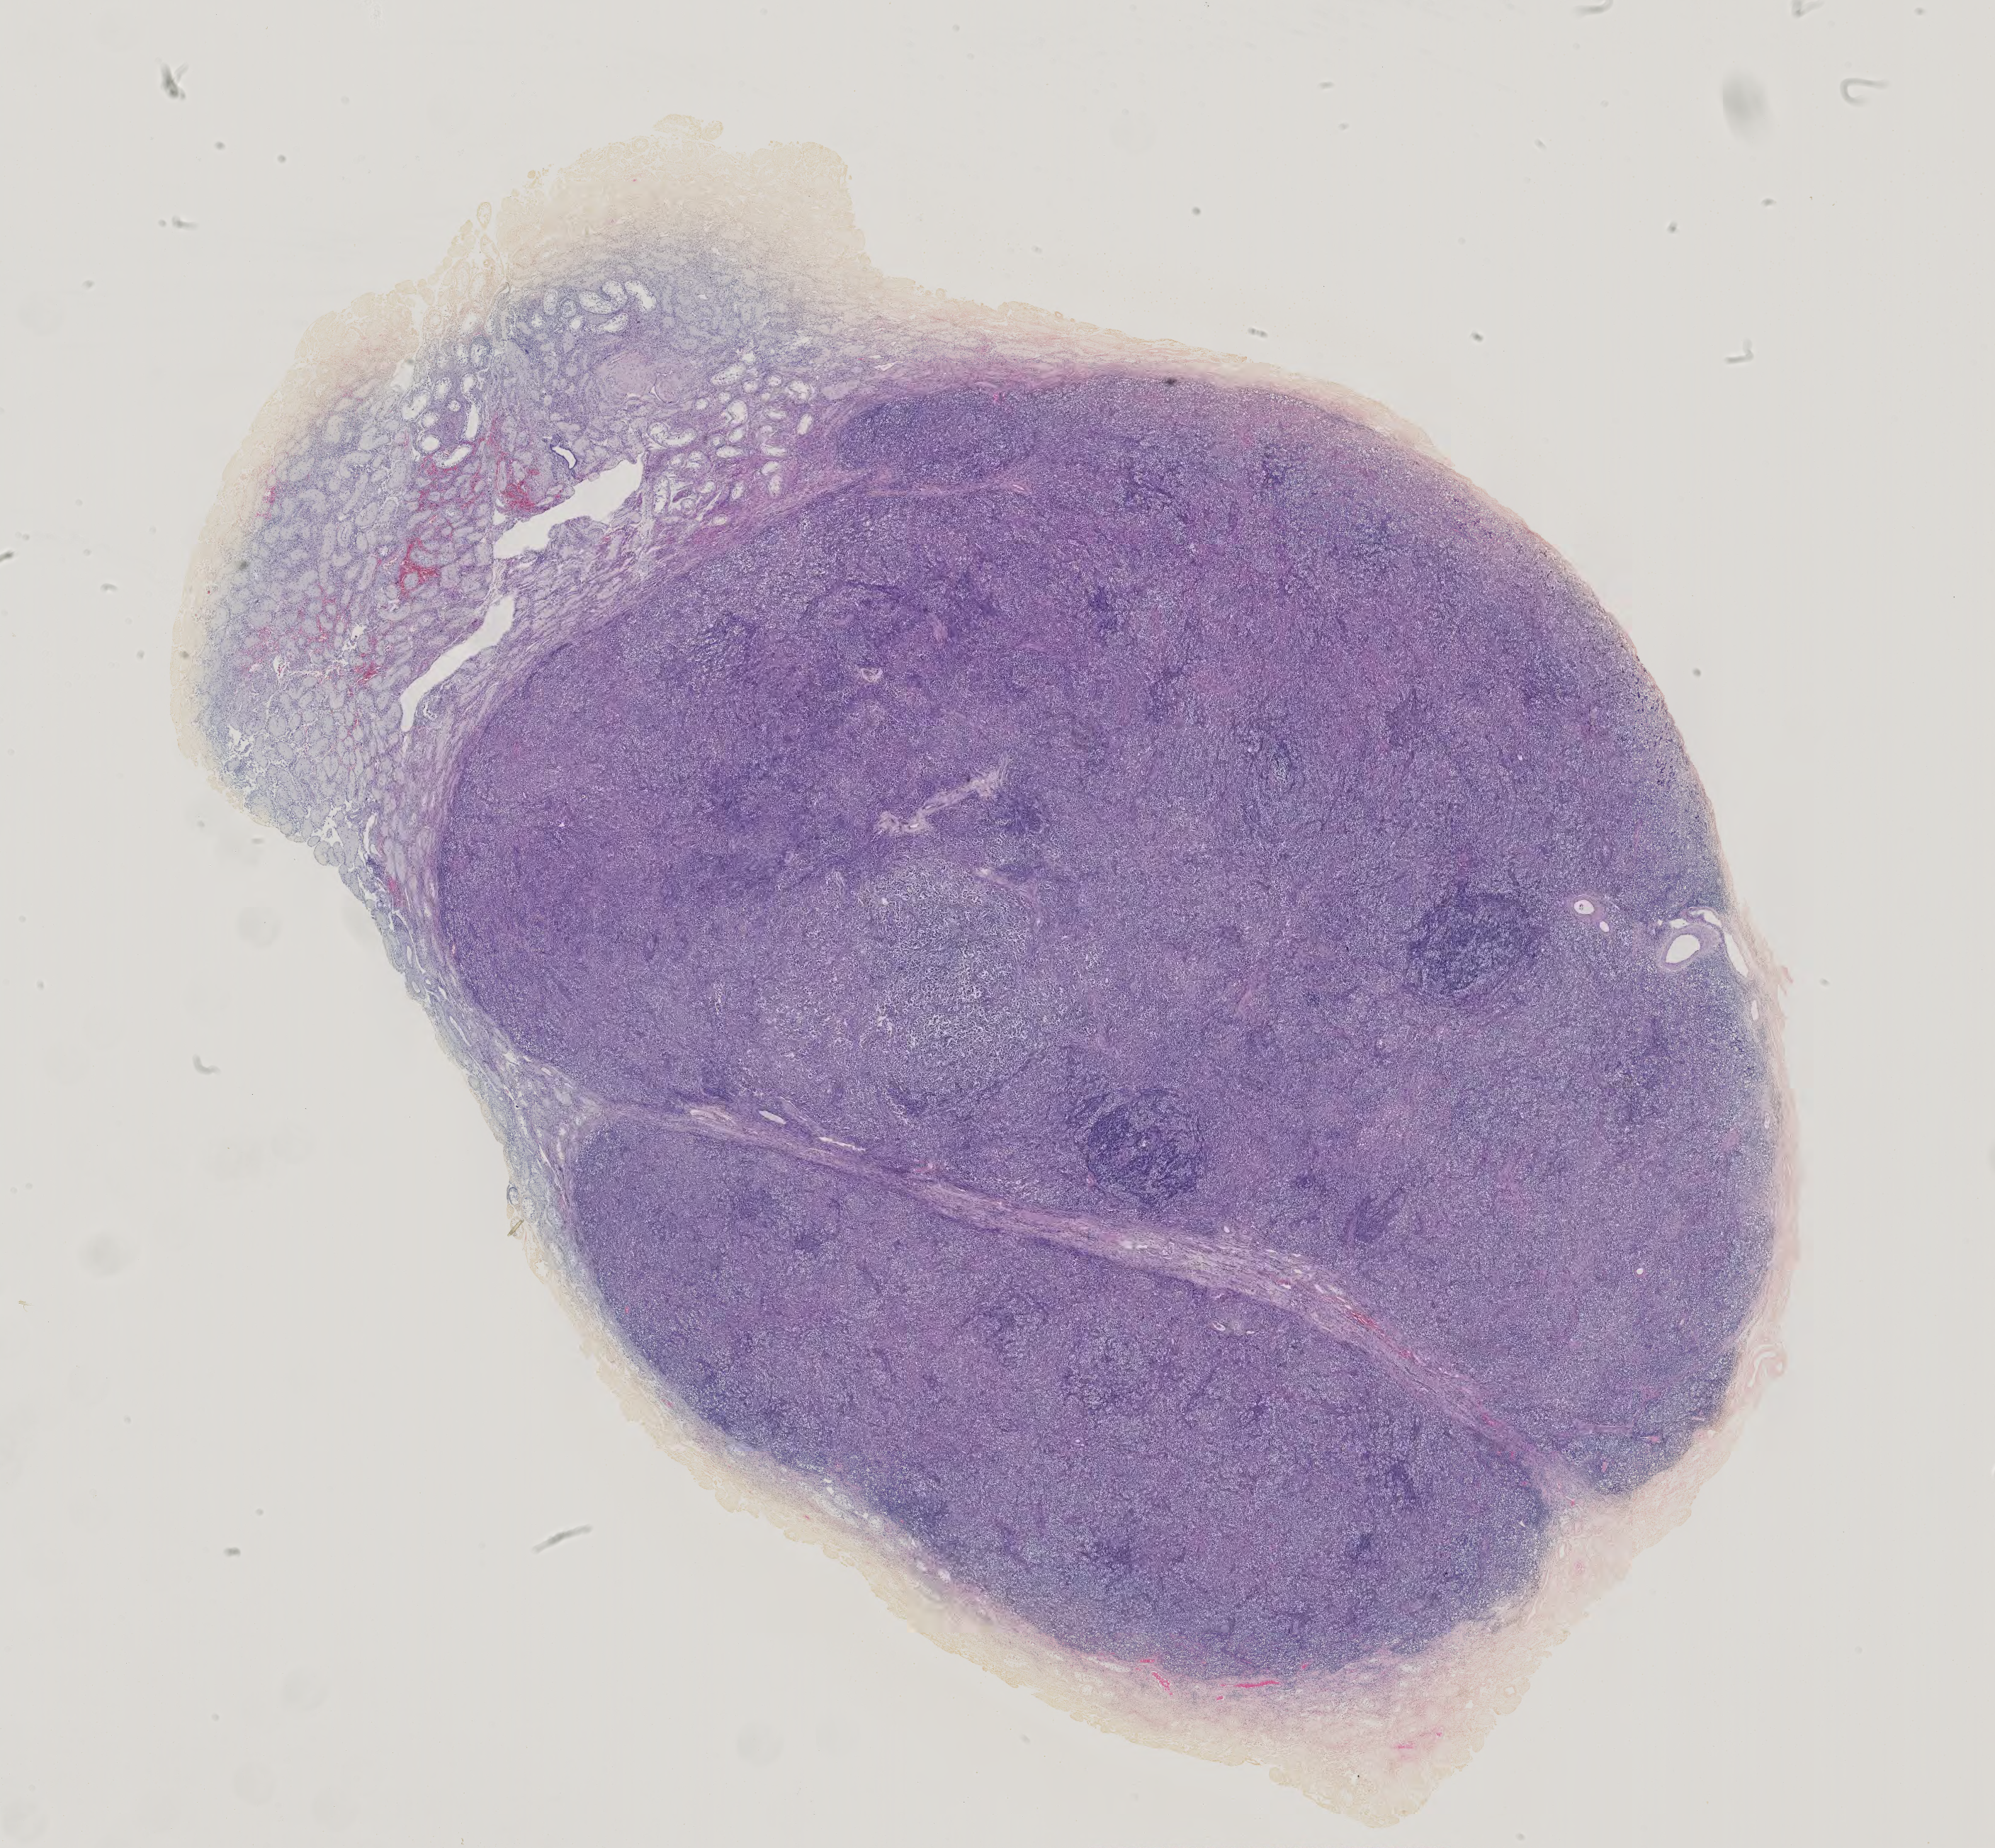
Digitized H&E-stained tissue section (whole slide) — shown as a low-resolution overview of the whole scanned area (about 20.5 x 19.0 mm, acquisition: 40x scan); formalin-fixed paraffin-embedded (FFPE) diagnostic section; additional new primary tumour sample from the testis. Male patient.
* this section: additional new primary tumour